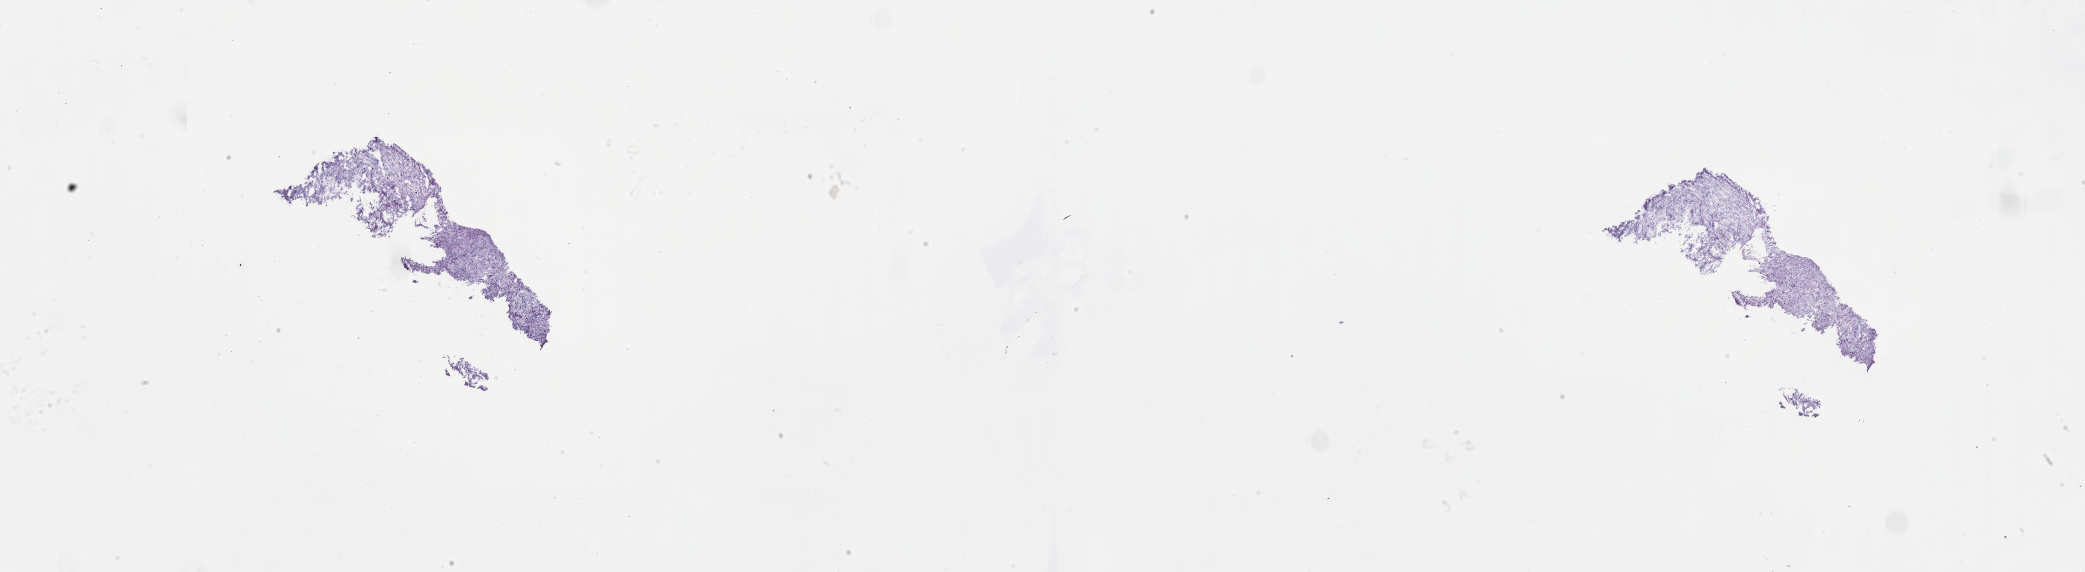
Whole-slide image, haematoxylin and eosin stain of tumor tissue from the cauda equina, a low-resolution overview of the entire scanned area, about 33.7 x 9.2 mm. Frozen section. Male patient, age 196 months (16 years 4 months).
• diagnosis (ICD-O-3 morphology term): Plasmacytoma, extramedullary